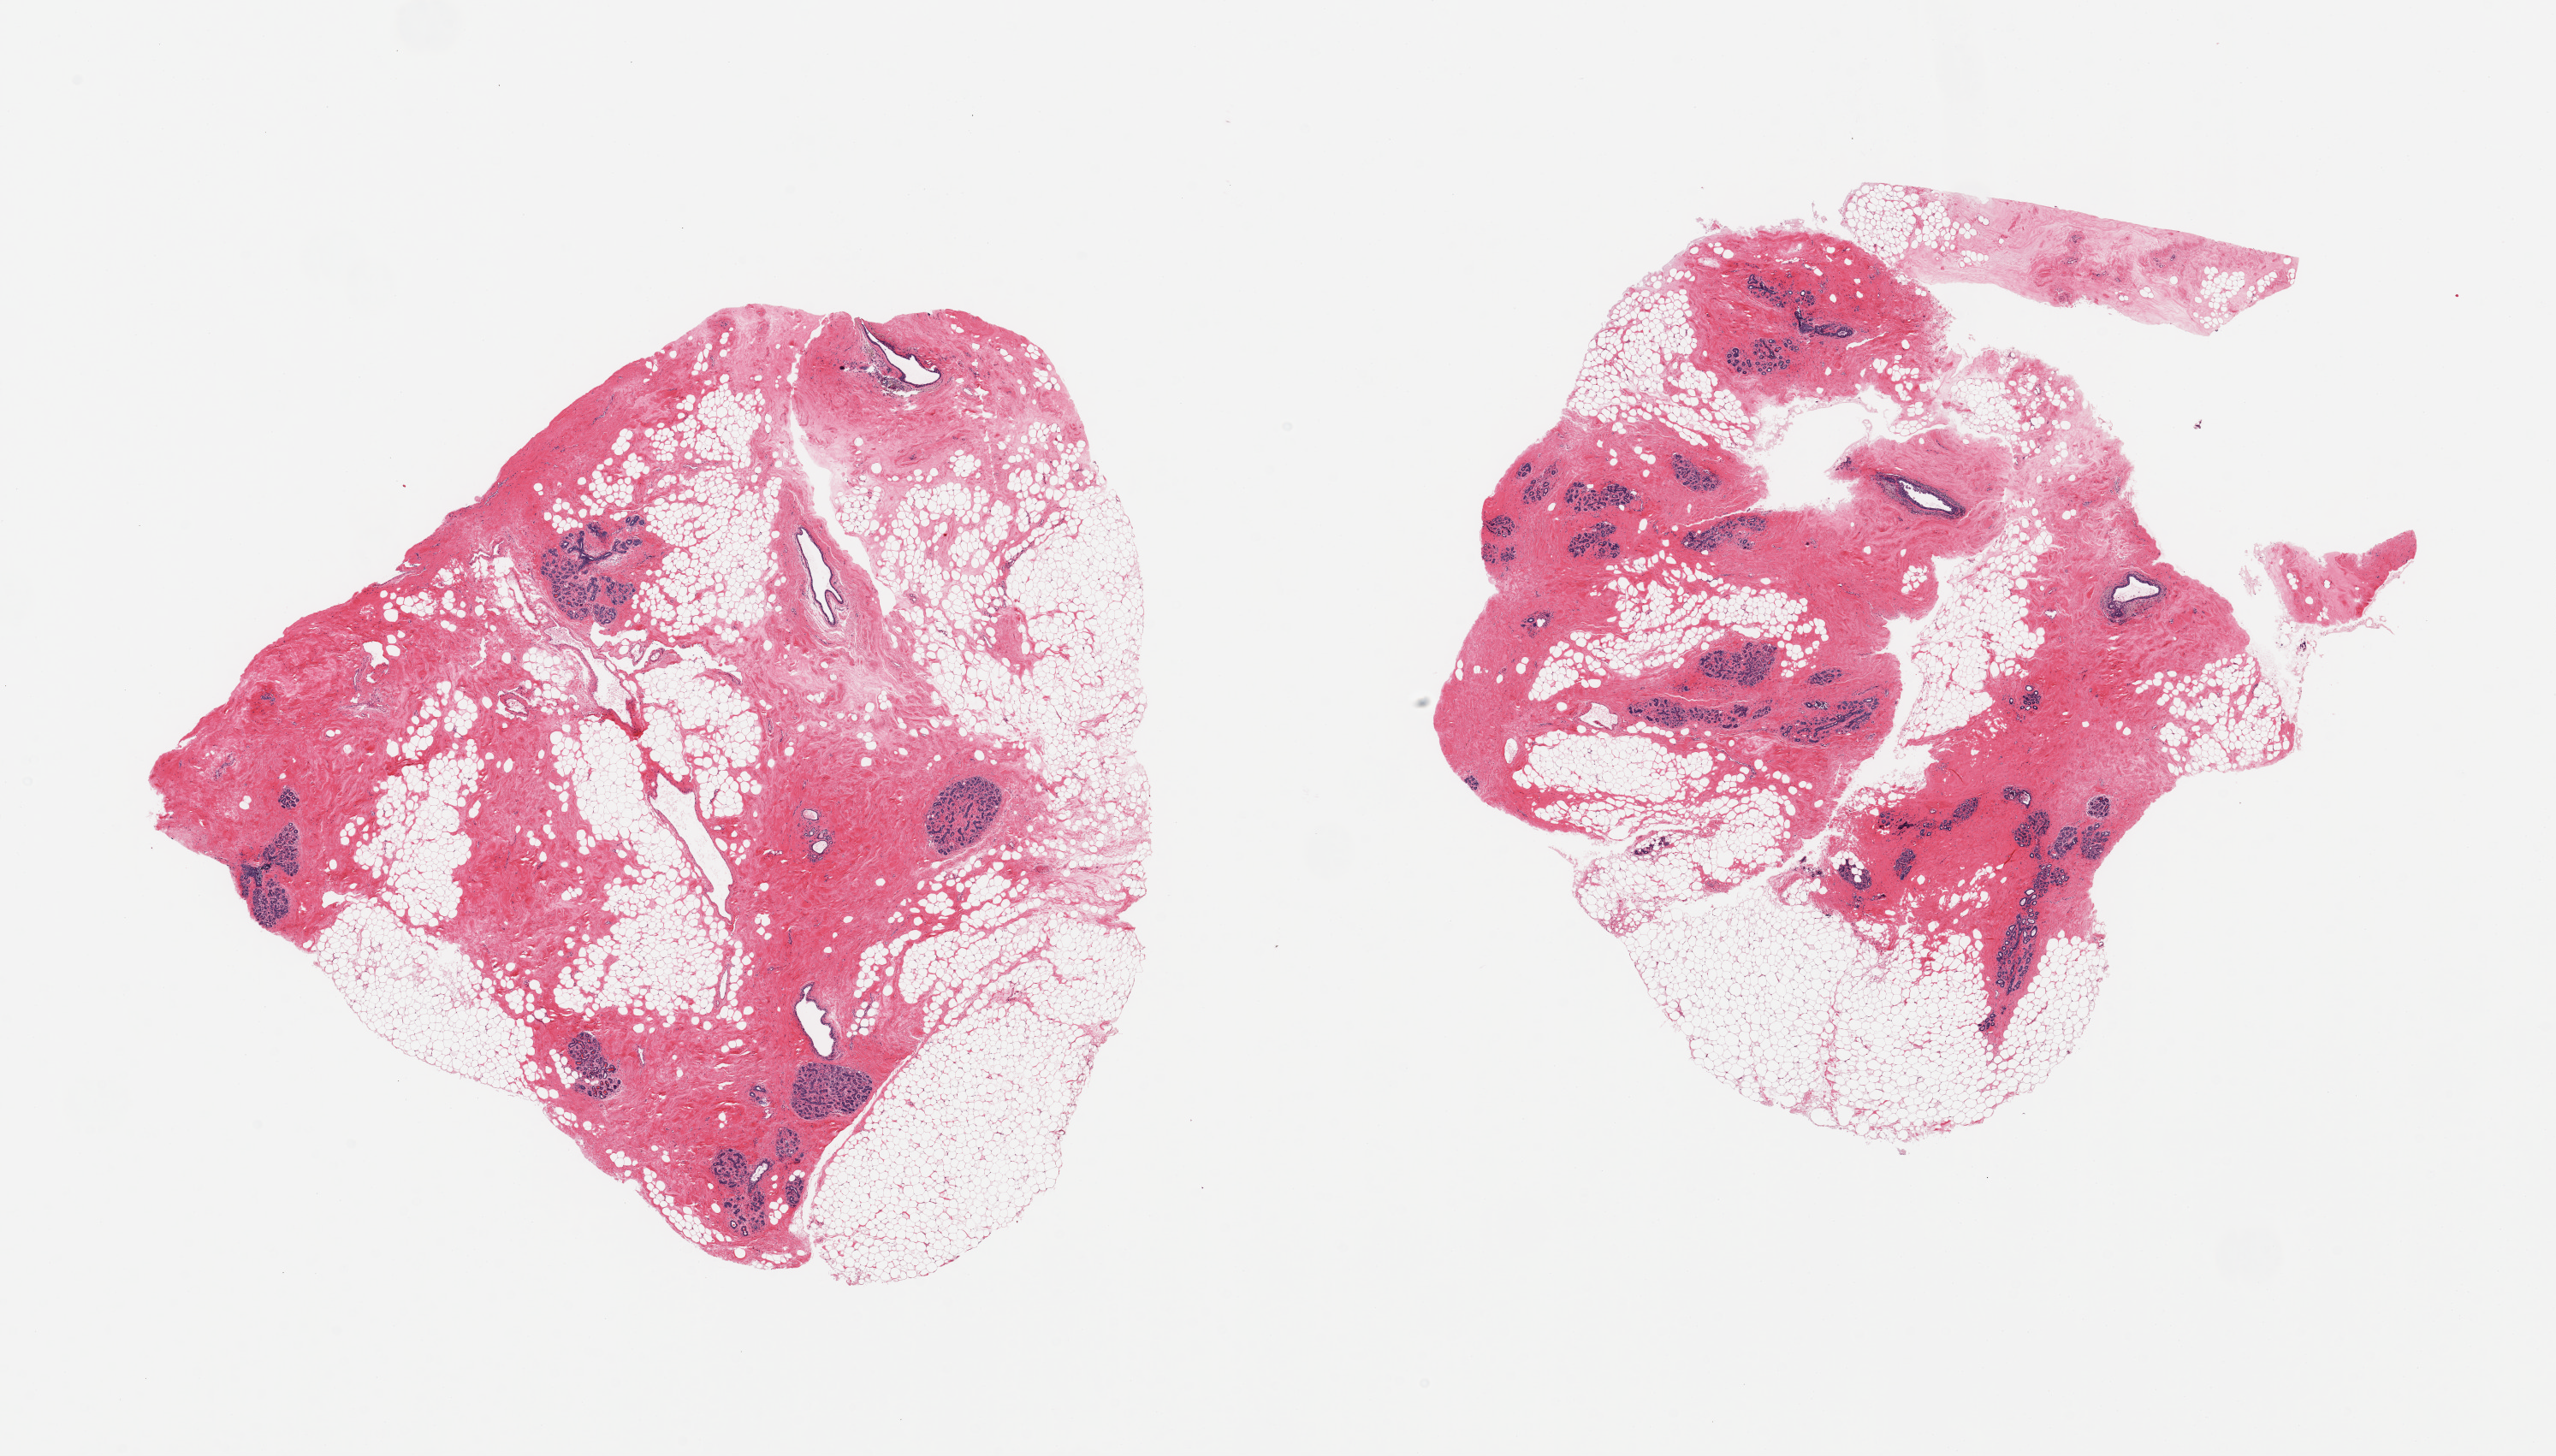
H&E whole-slide image — a low-resolution overview of the entire scanned area, about 23.6 x 13.5 mm (slide scanned at 20x). PAXgene-fixed paraffin-embedded (PFPE) section. Target tissue: breast. Tissue donor sample.
Pathologist's review note for this sample: 2 pieces, well- sampled normal duct and lobular units.